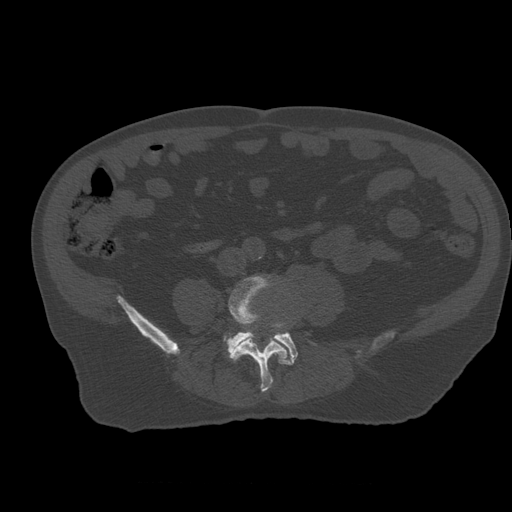
CT including the spine, one axial slice. Slice 155 of 399 in the series (ordered by position). 120 kVp. Bone window (W 1800 / L 400 HU). 512 × 512 image matrix. Patient age 73 years. Case-level facts recorded for this patient, not image findings: primary cancer: prostate; vertebrae with lytic lesions (as recorded): L2.
Structures marked on this image (semi-automatic segmentation, software-assisted and operator-edited):
- L4 vertebra: bounding box <224,276,287,393> (left, top, right, bottom; pixels)
- L5 vertebra: <227,324,298,365>